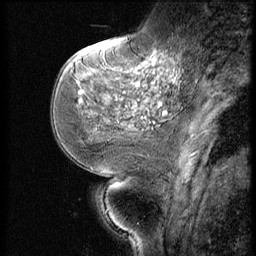
Breast MRI (dynamic contrast-enhanced), one sagittal slice; slice 21 of 56 in the series (ordered by position); dynamic contrast-enhanced series, image 2 of 3 at this slice position (ordered by acquisition); 1.5 T; TE 4.2 ms, TR 9 ms; 256 × 256 image matrix. Patient: female, 51 years. From the clinical record (not read from this slice): setting: breast cancer imaged before/during neoadjuvant chemotherapy; receptor status: triple-negative.
Outlined on this slice (semi-automatic segmentation, software-assisted and operator-edited):
- analysis volume of interest (the breast-tissue region the enhancement analysis was run in; not a lesion): box from (x=73, y=46) to (x=172, y=147) px
- tumour enhancement mask (voxels above the 140 % enhancement threshold inside the analysis volume of interest): (x=137, y=58)–(x=172, y=85)